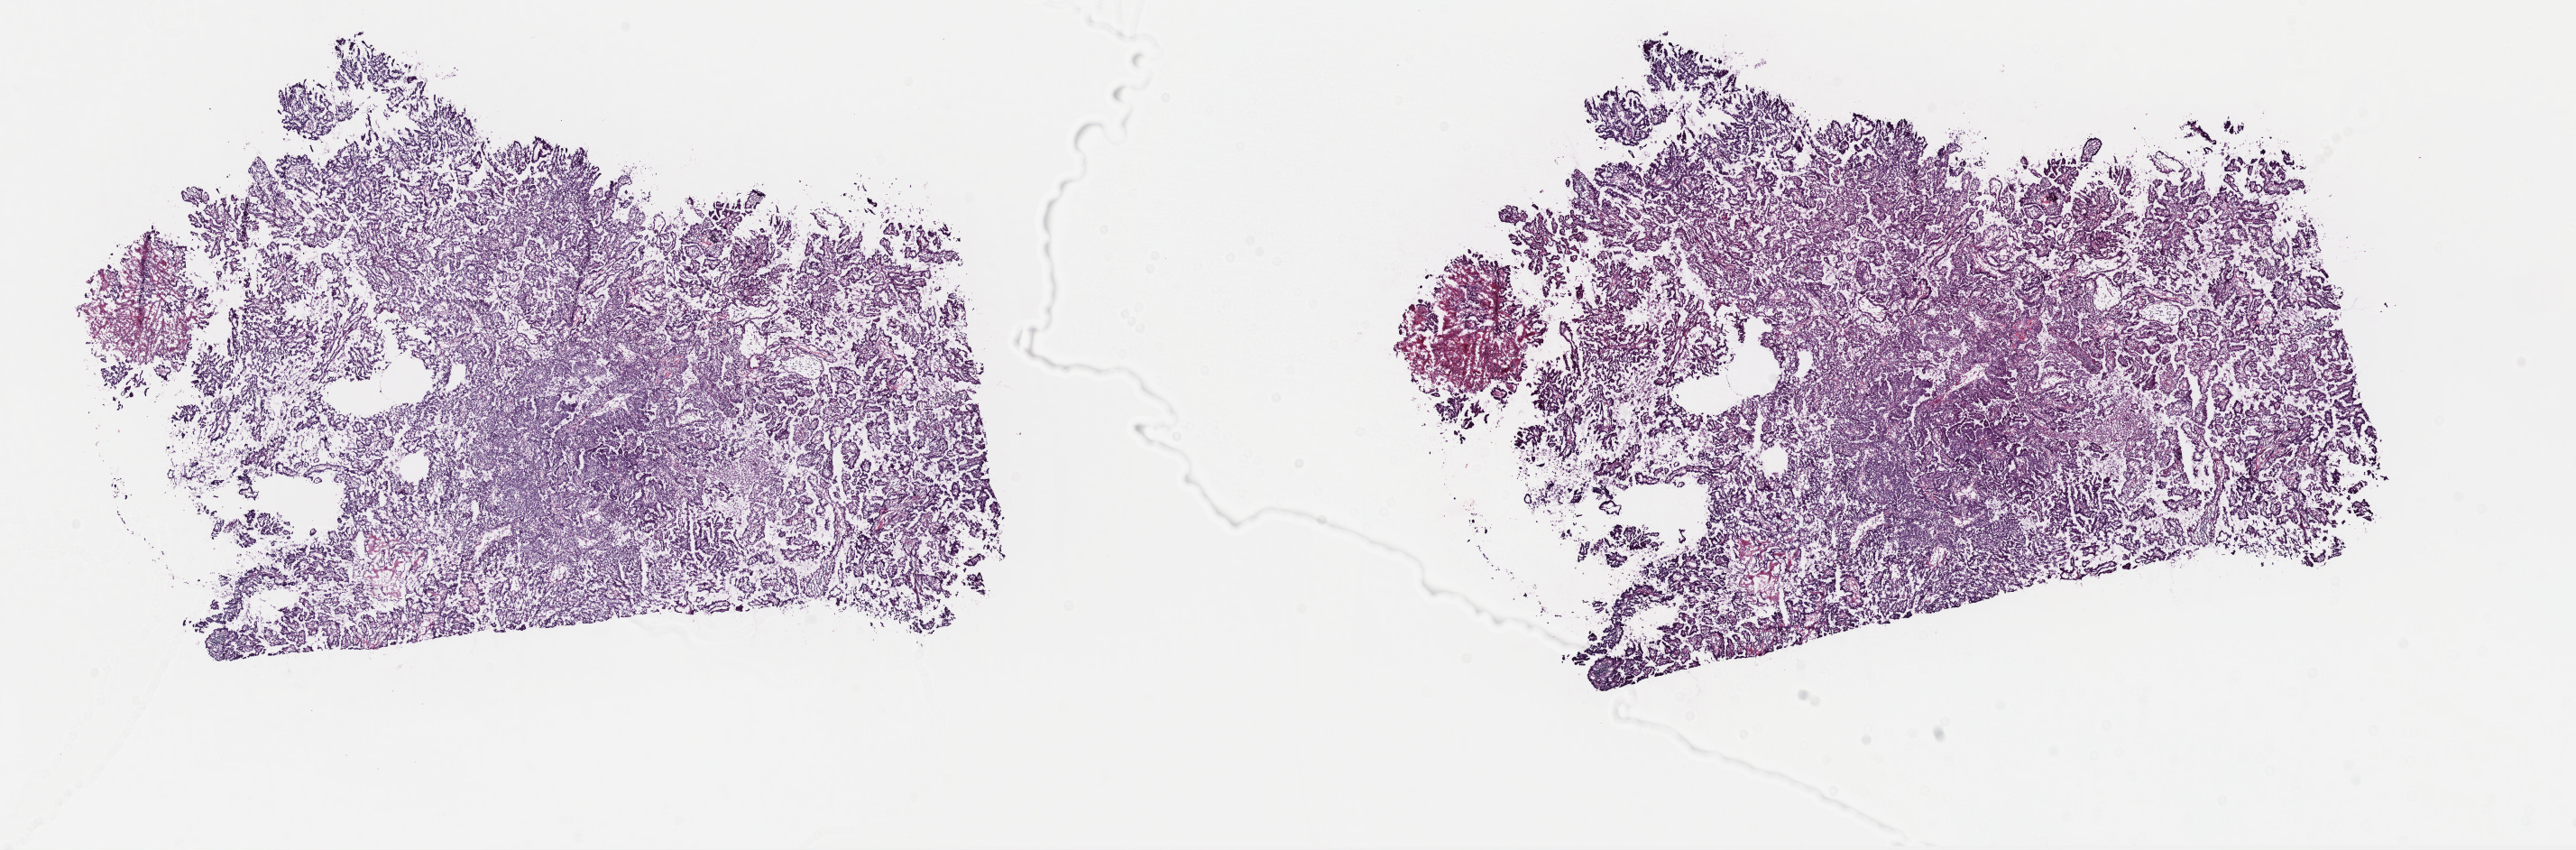
Digitized Hematoxylin and eosin (H&E) stained tissue section (whole slide) — a low-resolution overview of the entire scanned area, about 22.6 x 7.4 mm (acquisition: 40x scan). Frozen section from the top of the tissue portion. Uterus, primary tumour sample. Patient: female, age at initial diagnosis 57 years. Histologic grade: G3 (poorly differentiated). Slide review estimates, as recorded: tumour cells 90%, tumour nuclei 90%, normal cells 0%, stromal cells 0%, necrosis 10%. Inflammatory infiltration, as recorded: lymphocyte infiltration 40%, monocyte infiltration 20%, neutrophil infiltration 20%.
FIGO stage: IB. Diagnosis: Serous cystadenocarcinoma, NOS (endometrium).